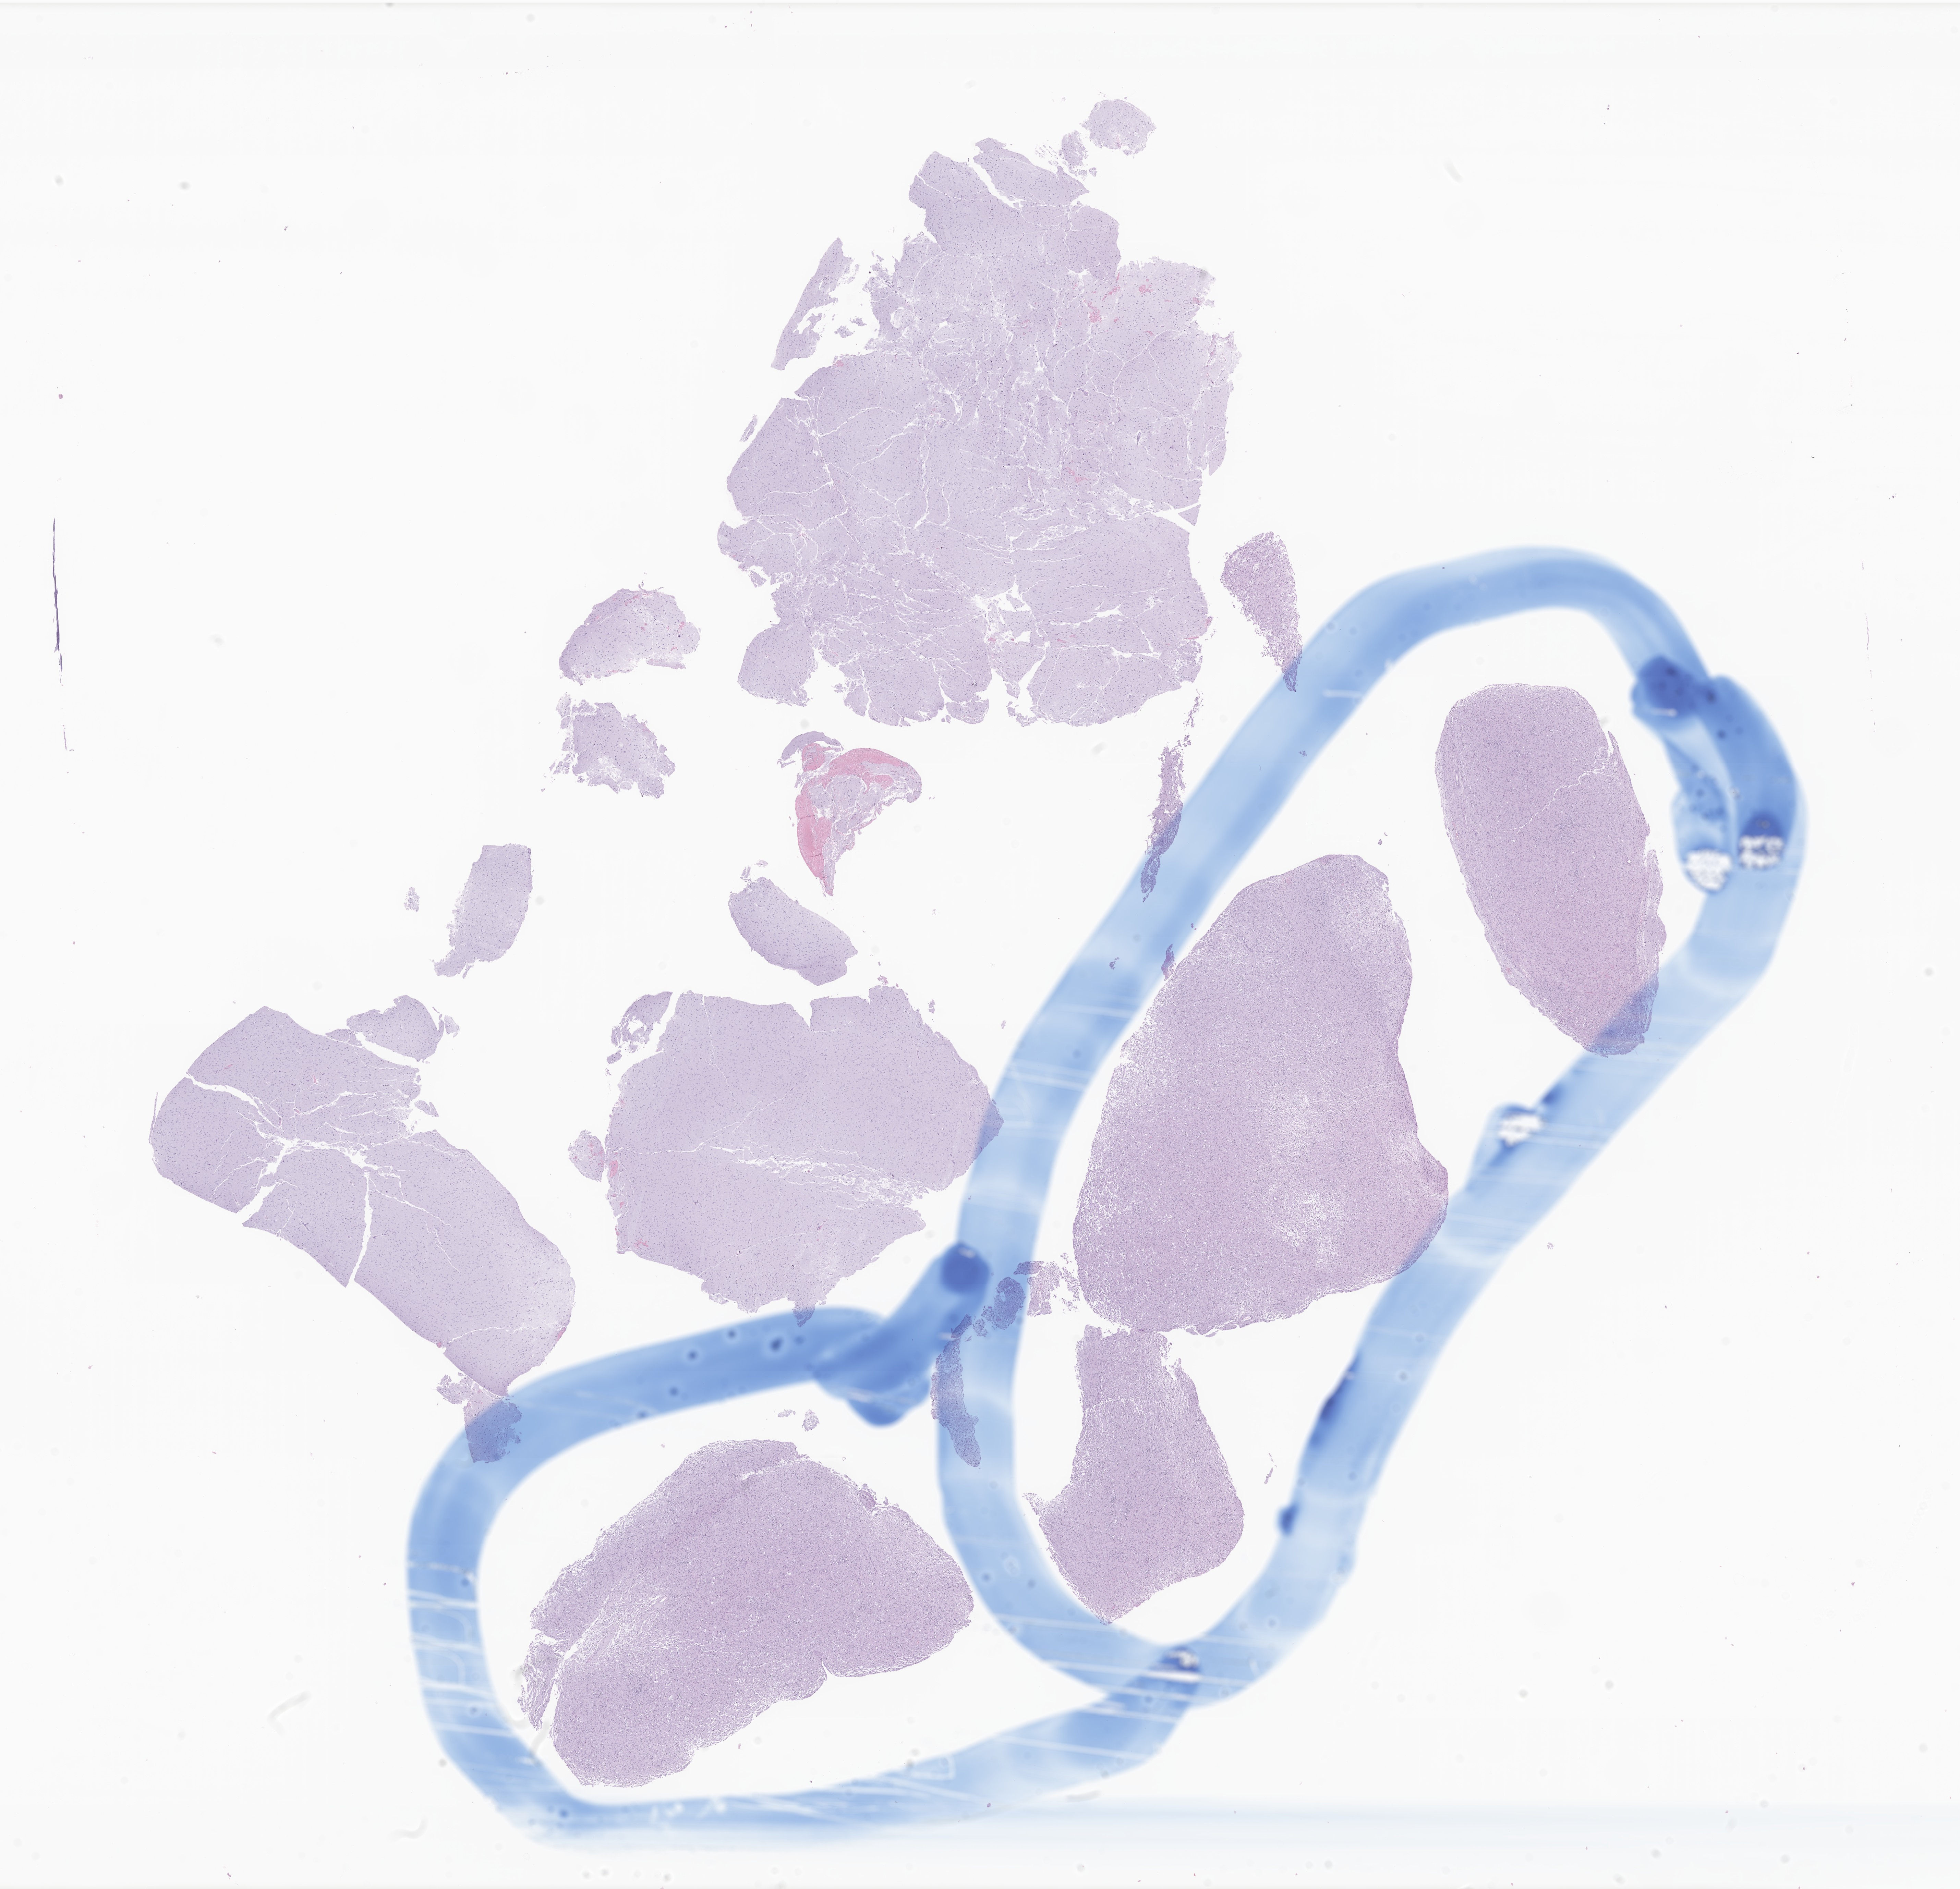
Whole-slide image, H&E stain of tumor tissue from the brain — low-resolution overview of the scanned area, about 24.1 x 23.2 mm, formalin-fixed paraffin-embedded section. Female patient, age 125 days.
Diagnosis (ICD-O-3 morphology term): Subependymal giant cell astrocytoma.